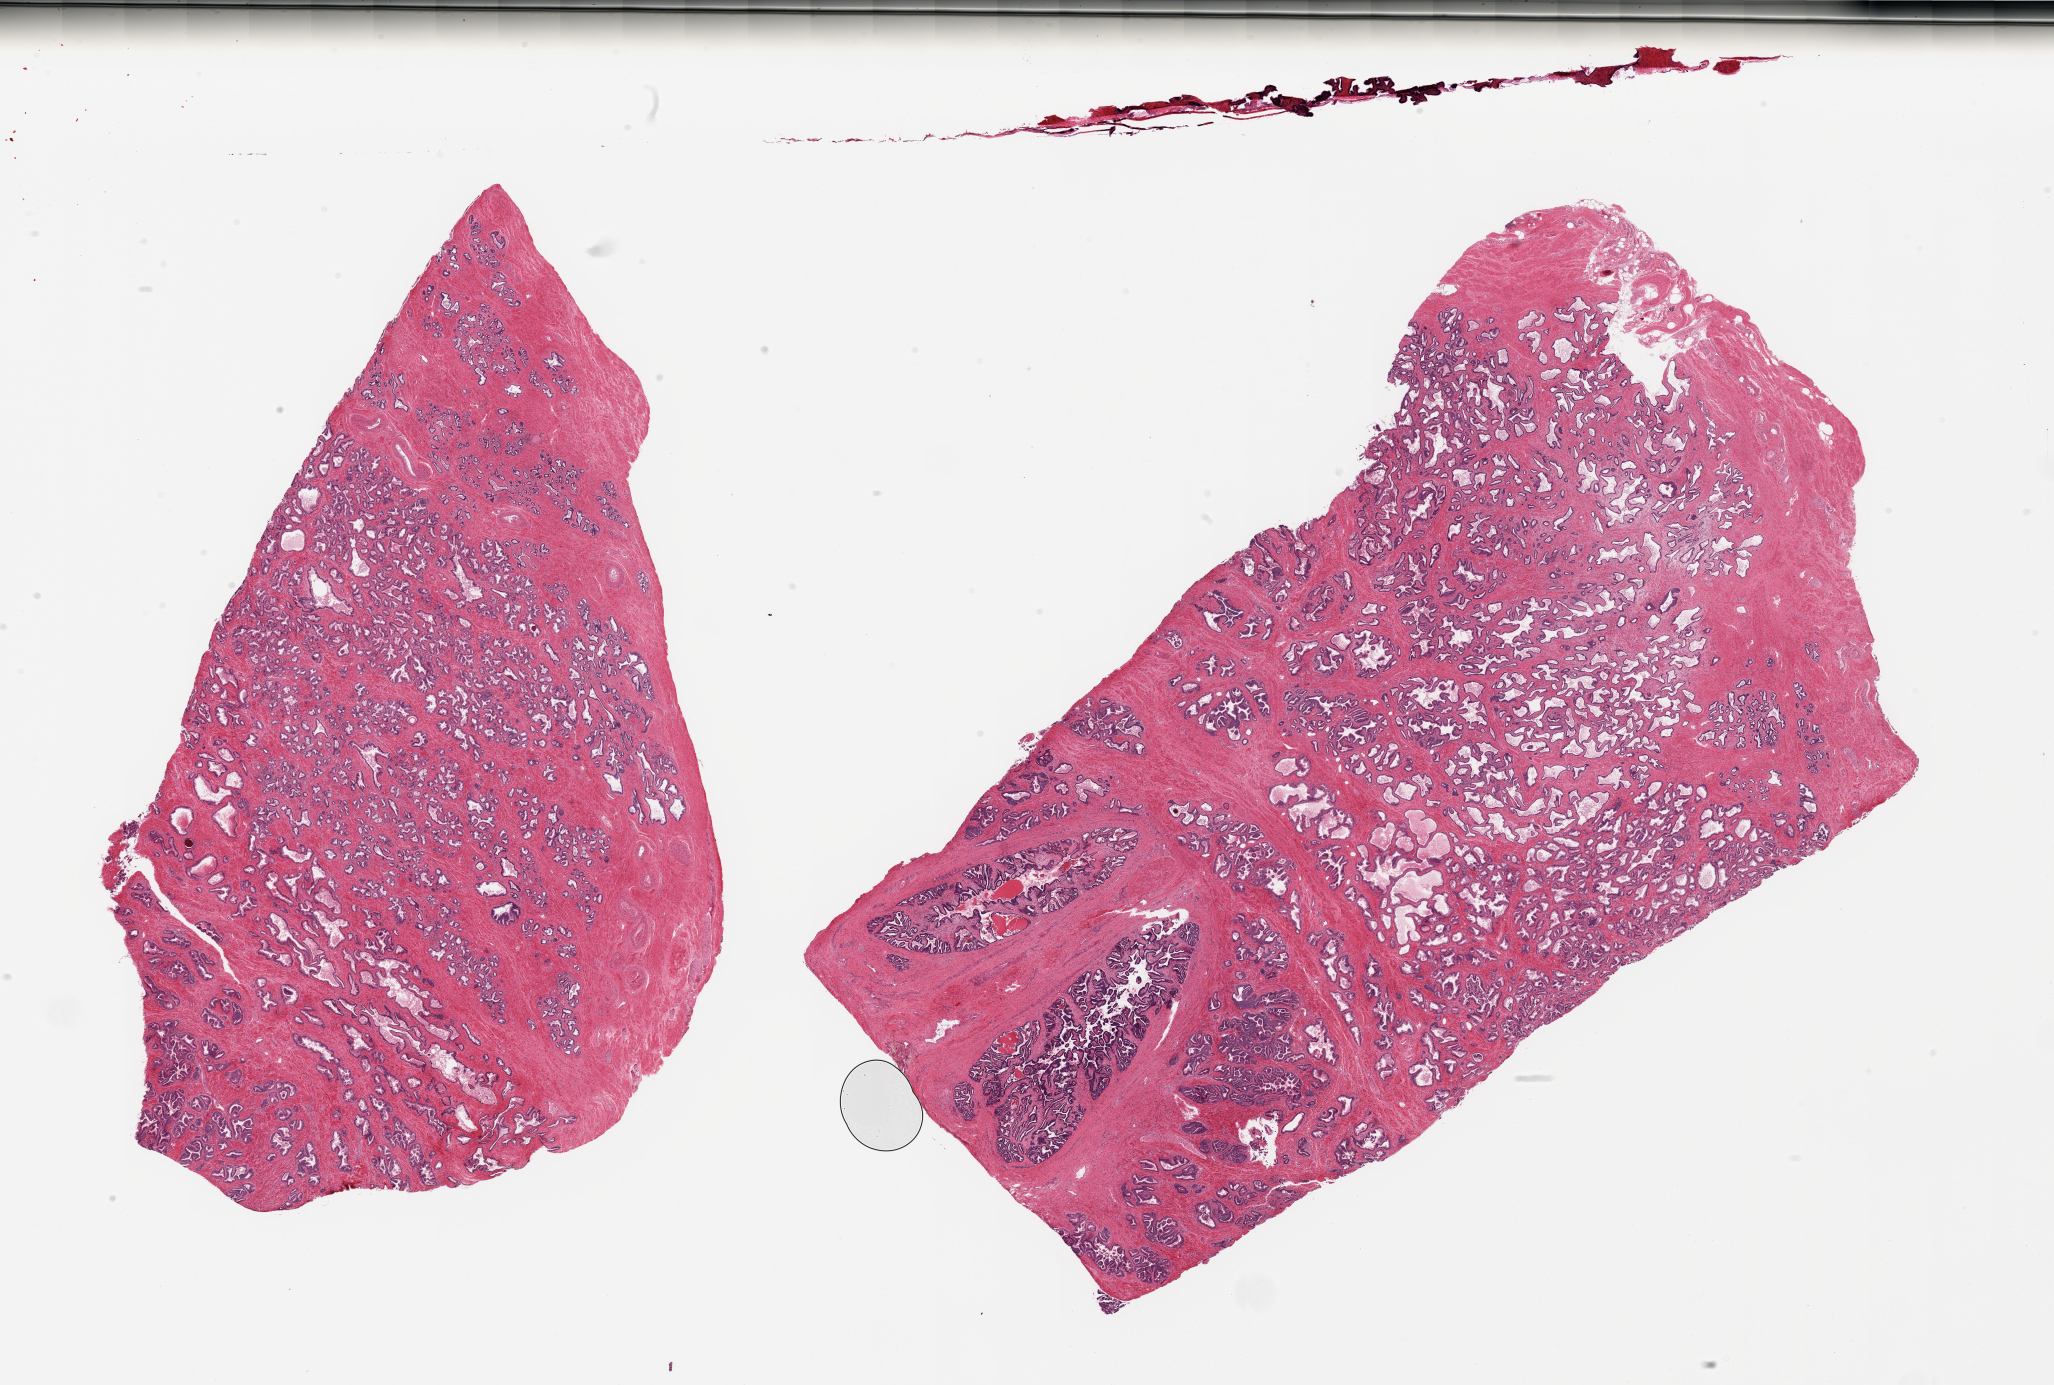
Hematoxylin and eosin (H&E) whole-slide image, whole scanned area (about 32.5 x 21.9 mm, from a 20x scan) shown as a low-resolution overview, PAXgene-fixed, paraffin-embedded tissue, section of prostate (target tissue), donor tissue sample. Donor: male.
Reviewer comment on this tissue sample: 2 pieces; seminal vesical occupies 25% of 1 piece.